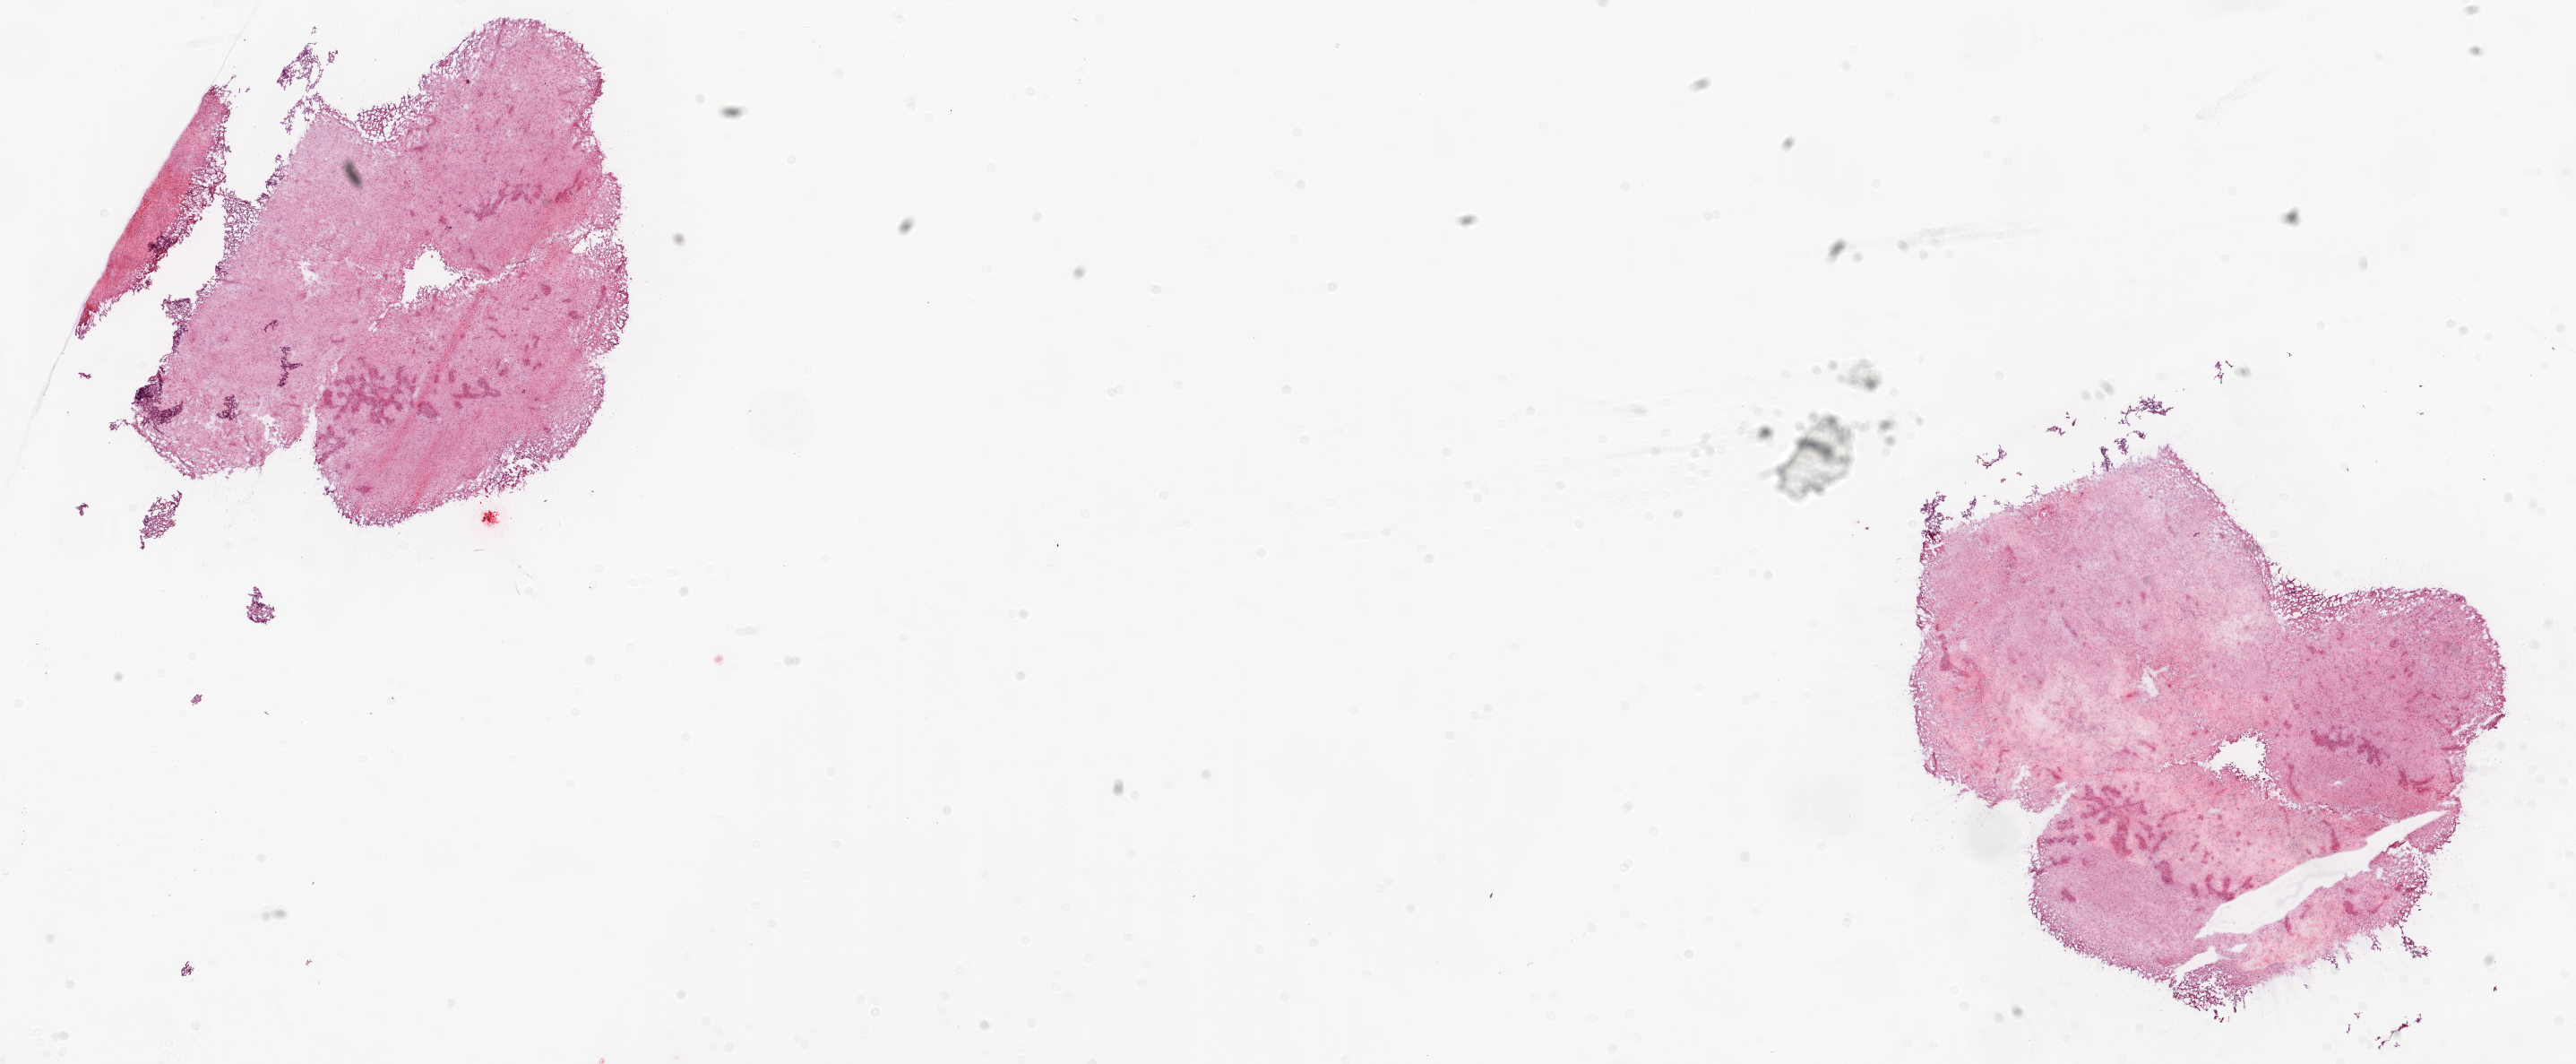
Digitized H&E tissue section (whole slide) — shown as a low-resolution overview of the whole scanned area (about 23.1 x 9.5 mm). Frozen section from the top of the tissue portion. Primary tumour sample from the brain. Patient: male, age at initial diagnosis 81 years. Composition of this section per pathologist review: tumour cells 50%, tumour nuclei 85%, normal cells 0%, stromal cells 0%, necrosis 50%.
Histologic diagnosis: Glioblastoma.